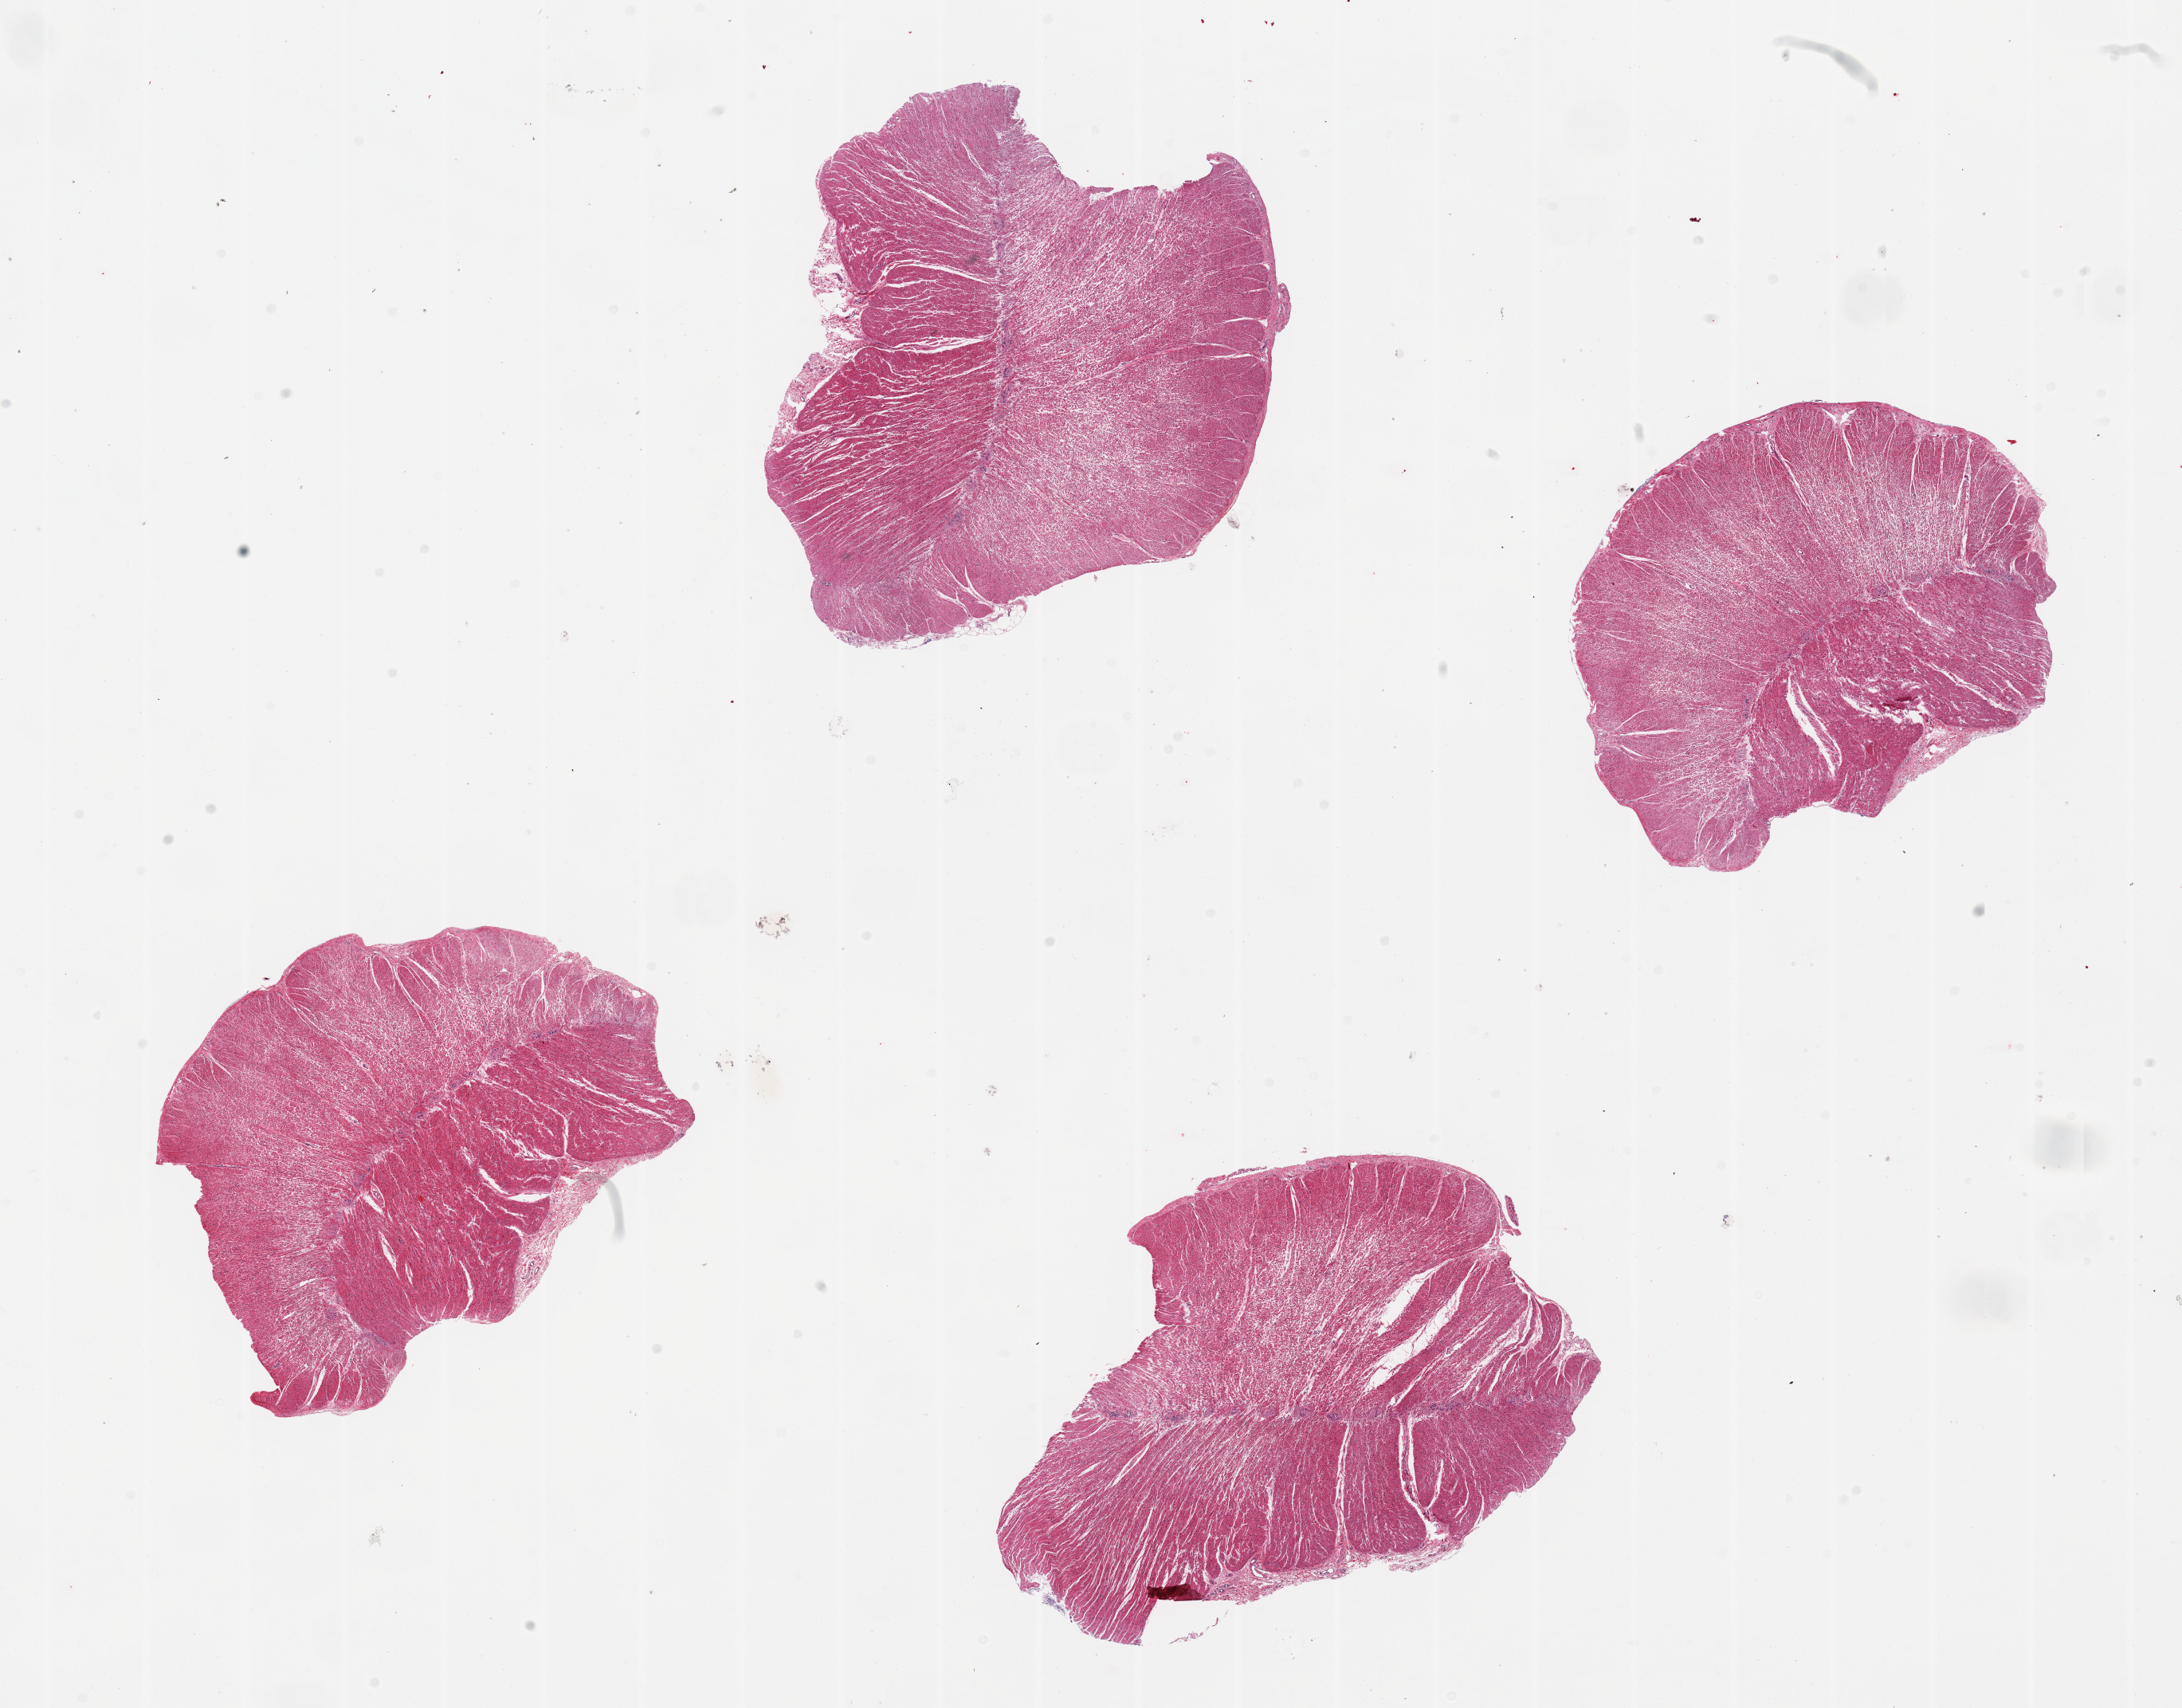
Digitized H&E-stained section — a low-resolution overview of the entire scanned area, about 21.7 x 17.0 mm, PAXgene-fixed, paraffin-embedded tissue, target tissue: sigmoid colon, tissue donor sample. Donor: female.
Pathologist's review note for this sample: 4 pieces.